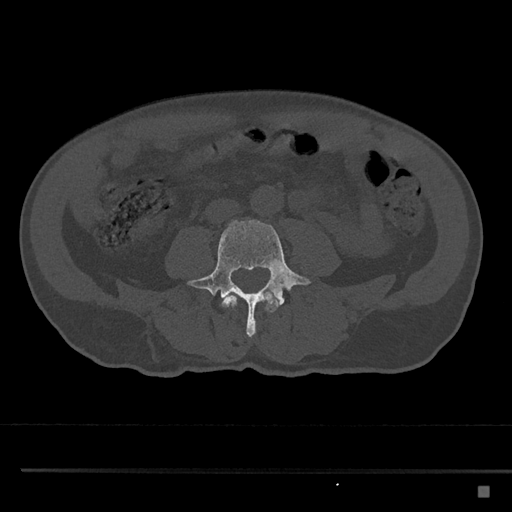
CT including the spine, one axial slice. Position 645 of 797 along the scan axis. Reconstruction kernel Br40s/3. Bone window (W 1800 / L 400 HU). 512 × 512 image matrix, field of view 391 × 391 mm. Patient: male, 59 years. From the clinical record (not read from this slice): primary cancer: prostate.
Annotated regions visible in this slice (semi-automatically segmented with operator editing):
- L3 vertebra: box from (x=222, y=291) to (x=278, y=319) px
- L4 vertebra: (x=187, y=219)–(x=310, y=338)